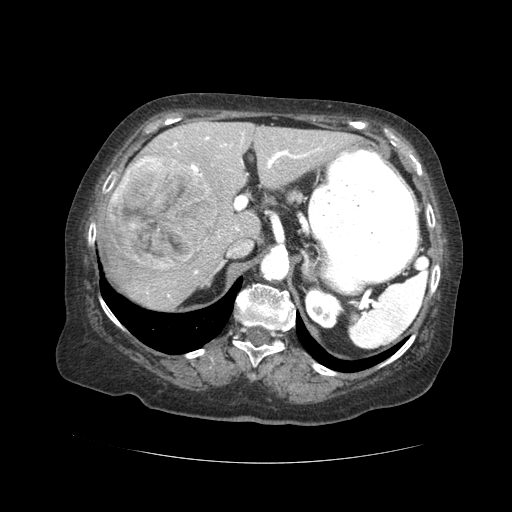
Contrast-enhanced abdominal CT (liver protocol), one axial slice; reconstruction kernel STANDARD; soft-tissue window (W 400 / L 40 HU); 512 × 512 image matrix, field of view 380 × 380 mm. From the clinical record (not read from this slice): diagnosis: hepatocellular carcinoma (patient treated with transarterial chemoembolisation; whether this scan precedes or follows treatment is not stated here); TNM stage (as recorded): Stage-I; Child-Pugh class: A; tumour nodularity: uninodular.
Annotated regions visible in this slice (semi-automatically segmented with operator editing):
- liver parenchyma outside the tumour (the mass and vessels are separate outlines, so this box may not span the whole liver): box from (x=98, y=120) to (x=356, y=310) px
- mass: (x=109, y=155)–(x=216, y=270)
- liver vessels: (x=167, y=133)–(x=322, y=297)